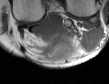
MRI of an extremity soft-tissue mass, one axial slice; MR volume resampled by the dataset authors to the PET/CT grid (not the native acquisition matrix); 109 × 84 image matrix, field of view 106 × 82 mm. Male patient. Case-level facts recorded for this patient, not image findings: histological type: synovial sarcoma; site of the primary tumour: left poplietal fossa.
Structures marked on this image (expert contour drawn on MRI and transferred to this co-registered scan by the dataset authors):
- gross tumour volume (mass): bounding box <57,39,74,59> (left, top, right, bottom; pixels)